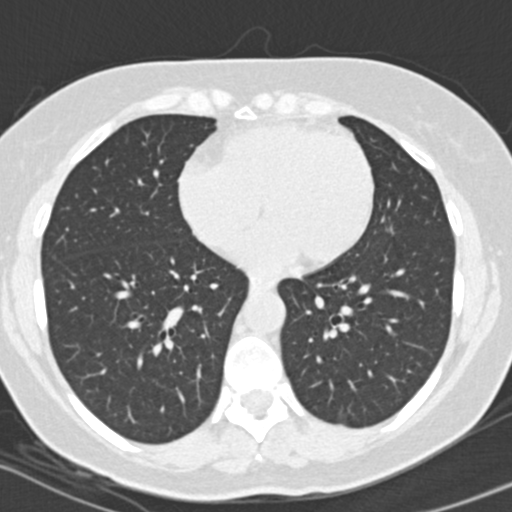
Chest CT (low-dose screening protocol), one axial image. Baseline annual screen. Lung window (W 1500 / L -600 HU). 2 mm slice thickness. Standard (soft-tissue) reconstruction kernel (B30f). Slice 94 of 151 in the series. Female participant, aged 56 years at enrolment. Former smoker at enrolment.
Lesion marked by an expert reader, bounding box <365,209,410,249> (left, top, right, bottom; pixels). Reader record for this screening exam (exam-level; its link to the box is not recorded): non-calcified nodule or mass ≥4 mm, lingula, 7 × 5 mm, smooth margins, soft tissue attenuation. Participant outcome: lung cancer diagnosed 863 days after this screen — adenocarcinoma, NOS, left upper lobe, poorly differentiated (G3), stage IIIA (AJCC 6th edition), 15 mm at pathology.